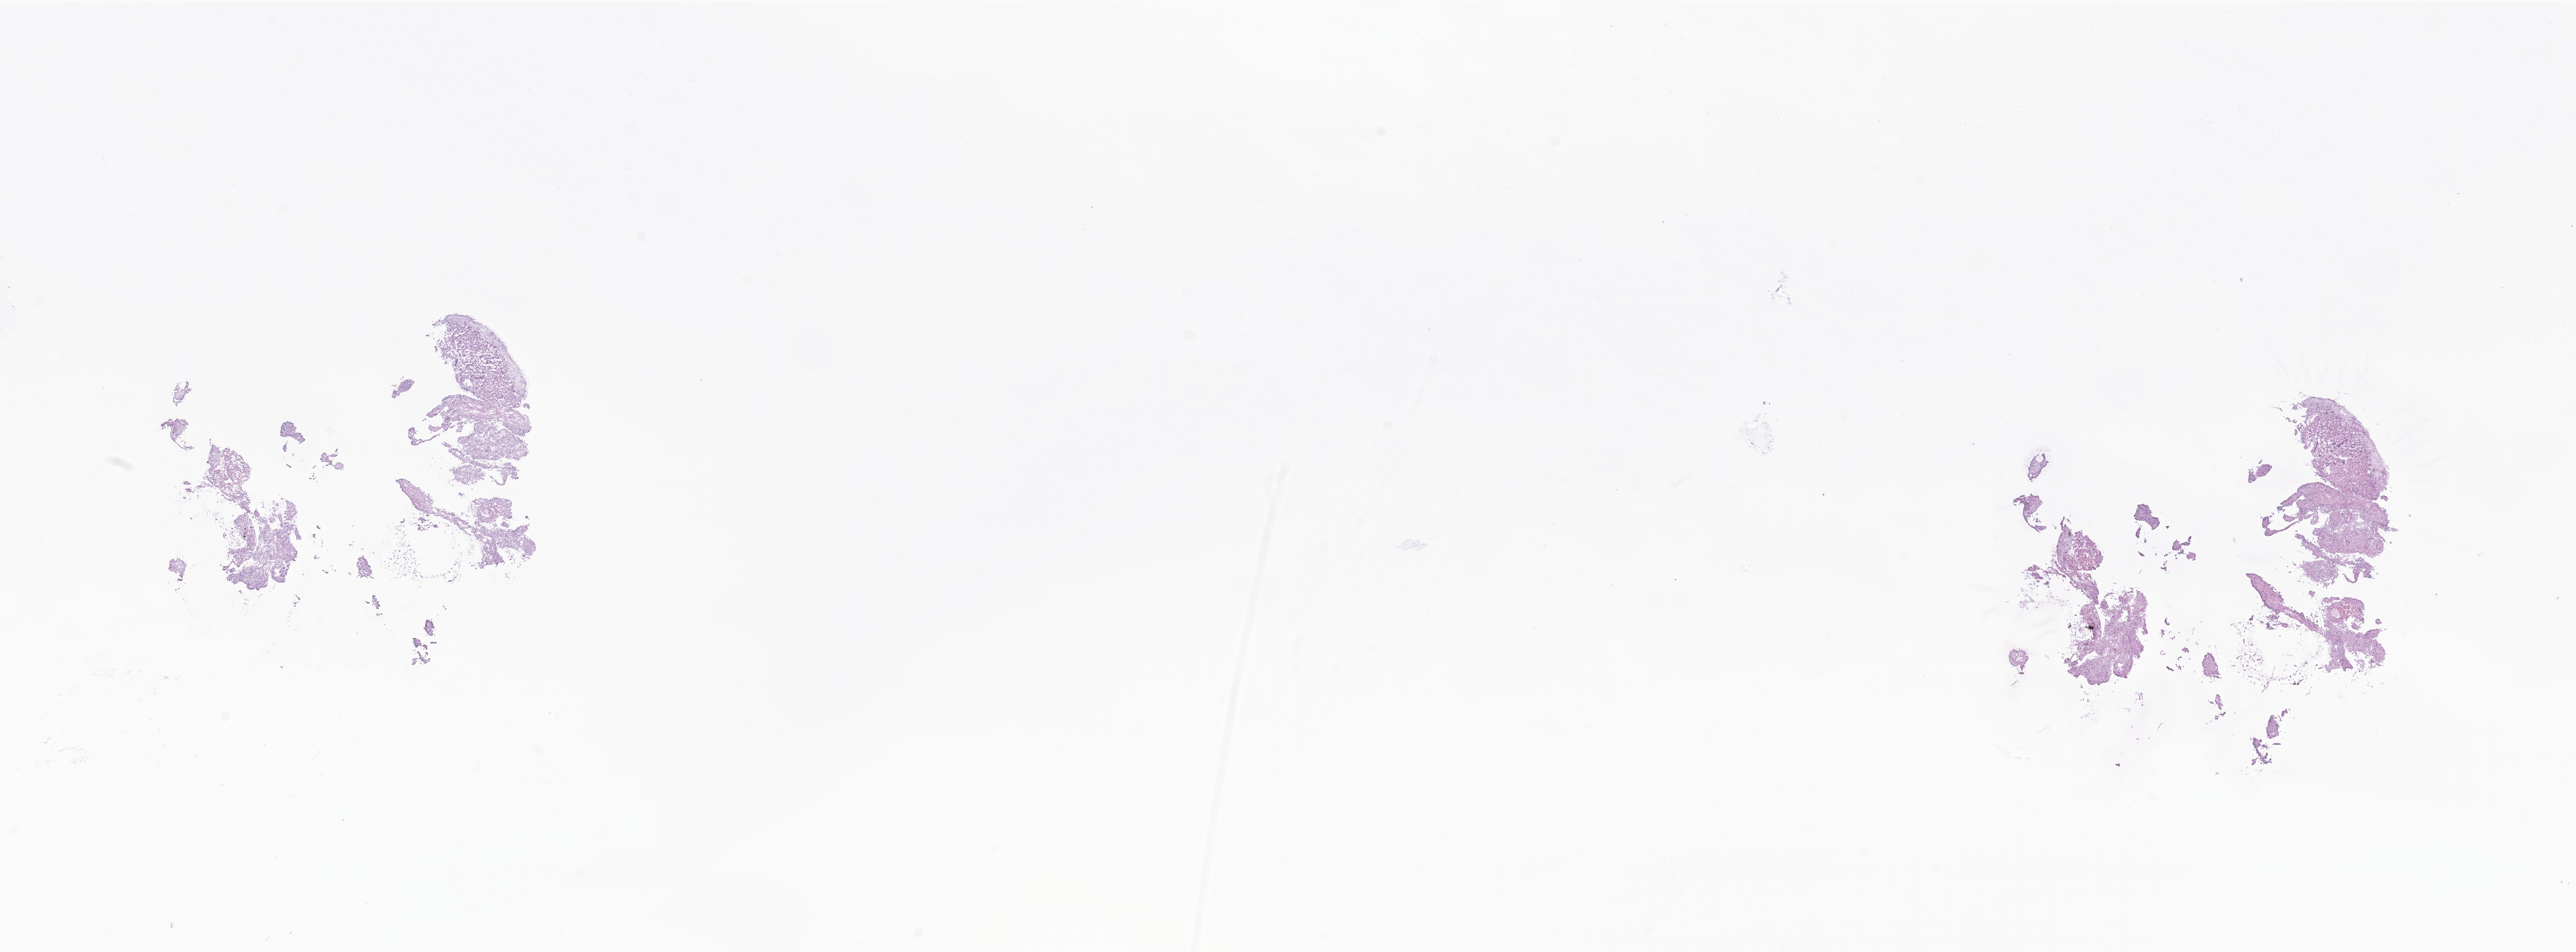
Whole-slide image, H&E stain of tumor tissue from the brain — whole scanned area (about 26.0 x 9.6 mm) shown as a low-resolution overview, cryosection (OCT / tissue freezing medium). Patient: female, age 216 months (18 years).
Diagnosis (ICD-O-3 morphology term): Neoplasm, uncertain whether benign or malignant.